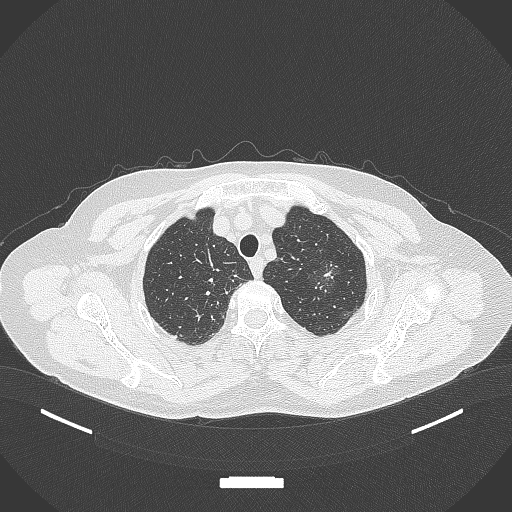
Chest CT, one axial slice; position 307 of 369 along the scan axis; lung window (W 1500 / L -600 HU); 512 × 512 image matrix, field of view 400 × 400 mm. Patient: female, 64 years. Case-level facts recorded for this patient, not image findings: clinical TNM (as recorded): T1c N0 M0.
Annotated regions visible in this slice (bounding box drawn by a radiologist):
- lung tumour (recorded histology: adenocarcinoma): bounding box (x1, y1, x2, y2) in pixels: (309, 256, 347, 294)